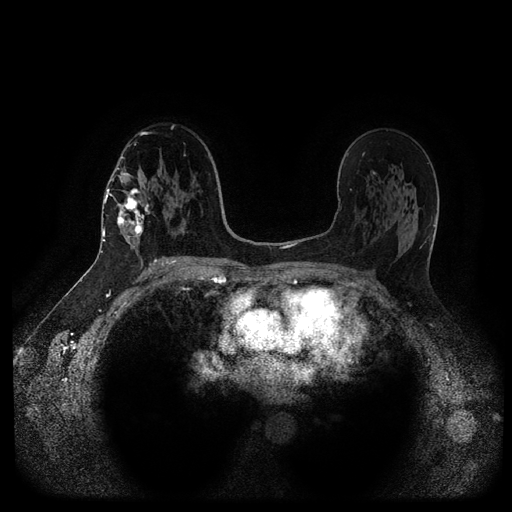
Breast MRI (dynamic contrast-enhanced, multi-phase), one axial slice. Position 60 of 116 along the scan axis. Dynamic contrast-enhanced series, time point 2 of 5 at this slice position (early post-contrast). 1.5 T. TE 2.6 ms, TR 5.3 ms. 2 mm slice thickness. 512 × 512 image matrix, field of view 360 × 360 mm. Female patient, age 58 years.
Outlined on this slice (semi-automatically segmented with operator editing):
- breast lesion (labelled 'tumour' in the annotation; benign lesions carry a separate 'benign' label): bounding box <114,185,153,244> (left, top, right, bottom; pixels)